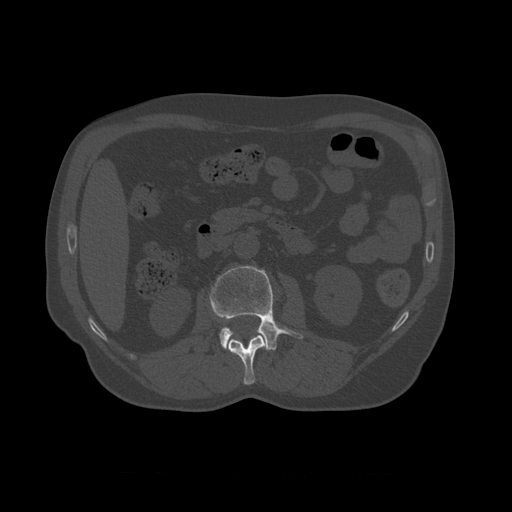
CT including the spine, one axial slice; position 341 of 450 along the scan axis; 120 kVp; bone window (W 1800 / L 400 HU); 1.25 mm slice thickness; 512 × 512 image matrix, field of view 405 × 405 mm. Patient age 75 years. From the clinical record (not read from this slice): primary cancer: prostate.
Structures marked on this image (semi-automatic segmentation, software-assisted and operator-edited):
- L1 vertebra: bounding box (x1, y1, x2, y2) in pixels: (228, 335, 270, 385)
- L2 vertebra: (210, 266, 304, 351)